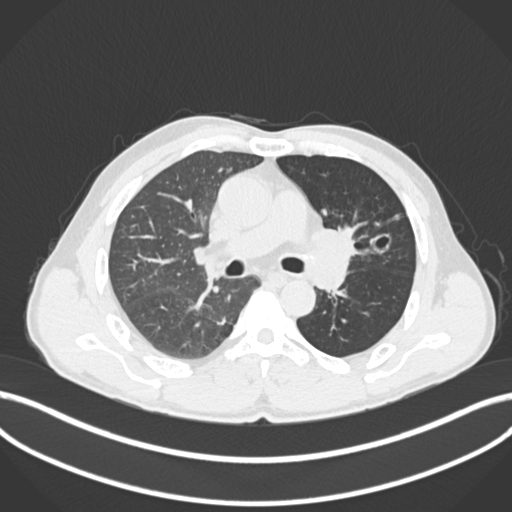
Chest CT, one axial slice. Position 113 of 255 along the scan axis. Reconstruction kernel B30f. 120 kVp. Lung window (W 1500 / L -600 HU). 1 mm slice thickness. 512 × 512 image matrix, field of view 400 × 400 mm. Patient: male, 57 years. From the clinical record (not read from this slice): clinical TNM (as recorded): T2b N0 M0.
Structures marked on this image (bounding box drawn by a radiologist):
- lung tumour (recorded histology: squamous cell carcinoma): bounding box (x1, y1, x2, y2) in pixels: (310, 217, 373, 261)